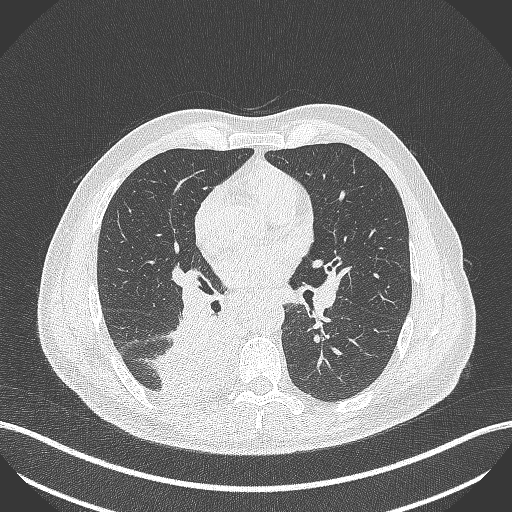
Chest CT, one axial slice. Slice 247 of 451 in the series (ordered by position). Reconstruction kernel B70f. 100 kVp. Lung window (W 1500 / L -600 HU). 512 × 512 image matrix, field of view 400 × 400 mm. Patient: male, 61 years. From the clinical record (not read from this slice): clinical TNM (as recorded): T1 N0 M0; histopathological grade: G3.
Outlined on this slice (bounding box drawn by a radiologist):
- lung tumour (recorded histology: small cell carcinoma): bounding box [x1, y1, x2, y2] px = [154, 304, 234, 398]